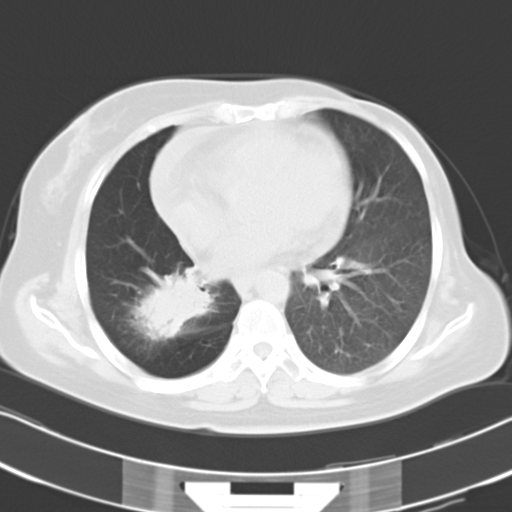
Chest CT, one axial slice; position 14 of 30 along the scan axis; reconstruction kernel B40f; 120 kVp; lung window (W 1500 / L -600 HU); 8 mm slice thickness; 512 × 512 image matrix. Female patient, age 53 years. Case-level facts recorded for this patient, not image findings: clinical TNM (as recorded): T2b N1 M0.
Outlined on this slice (rectangle marked by the reading radiologist):
- lung tumour (recorded histology: adenocarcinoma): box from (x=134, y=274) to (x=216, y=338) px